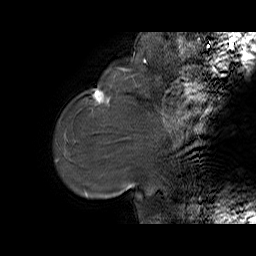
Breast MRI (dynamic contrast-enhanced), one sagittal slice; dynamic contrast-enhanced series, time point 2 of 6 at this slice position (early post-contrast); 1.5 T; TE 5.7 ms, TR 32.9 ms; 4 mm slice thickness; 256 × 256 image matrix. Female patient. Case-level facts recorded for this patient, not image findings: setting: breast cancer imaged before/during neoadjuvant chemotherapy; receptor status: HER2-positive.
Structures marked on this image (semi-automatic segmentation, software-assisted and operator-edited):
- analysis volume of interest (the breast-tissue region the enhancement analysis was run in; not a lesion): bounding box [x1, y1, x2, y2] px = [79, 77, 125, 126]
- tumour enhancement mask (voxels above the 100 % enhancement threshold inside the analysis volume of interest): [94, 90, 109, 103]